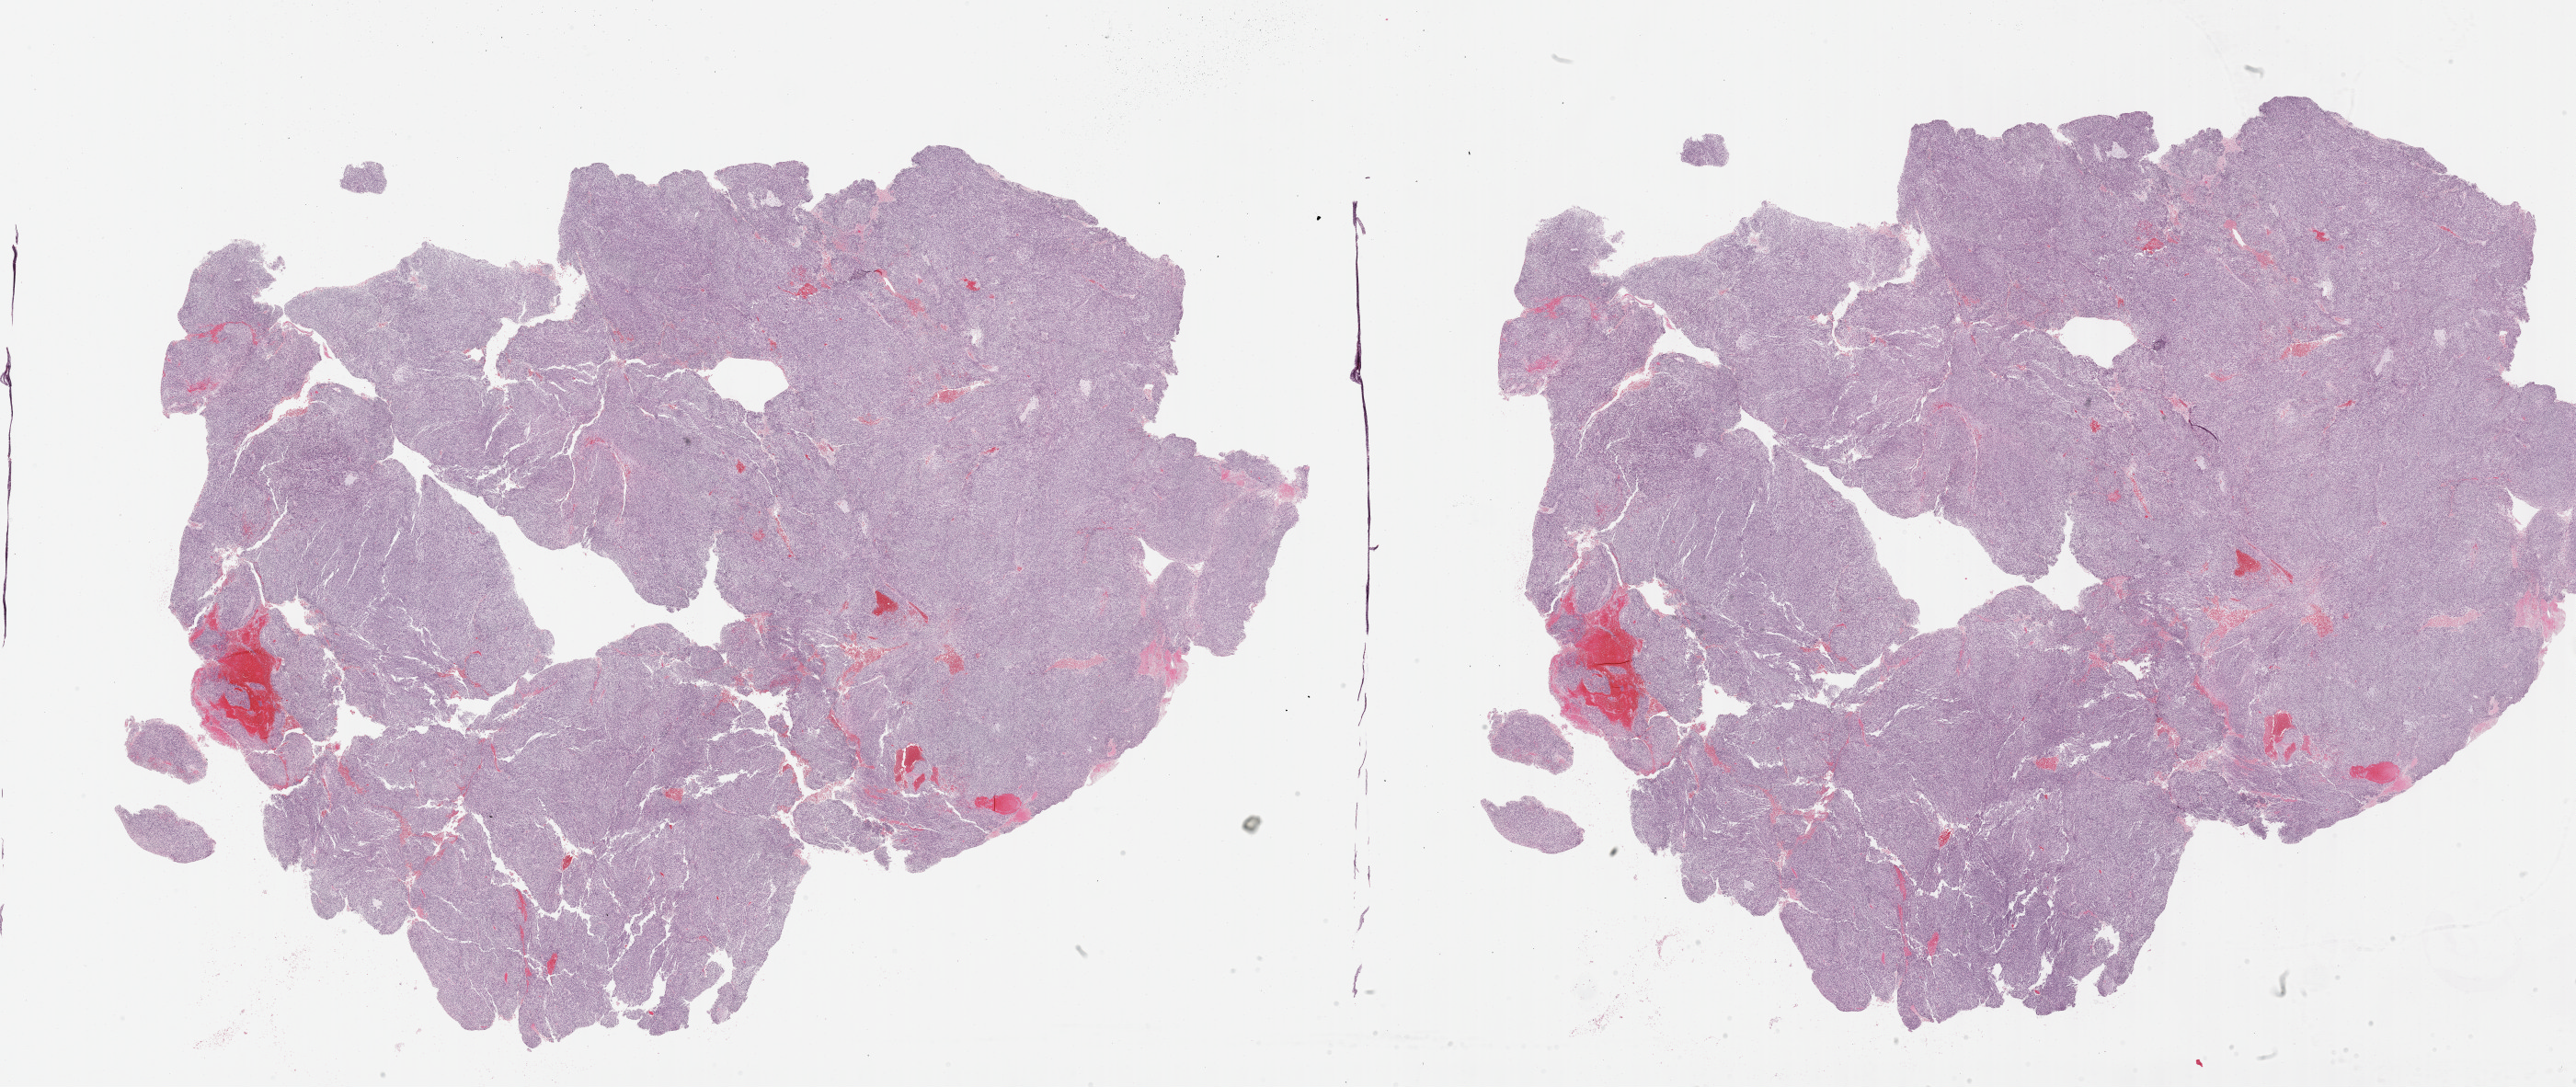
H&E-stained whole-slide image, a low-resolution overview of the entire scanned area, about 45.3 x 19.1 mm; formalin-fixed paraffin-embedded (FFPE) diagnostic section; primary tumour sample from the retroperitoneum and peritoneum. Female patient; age at initial diagnosis 53 years.
* diagnosis: Leiomyosarcoma, NOS (retroperitoneum)